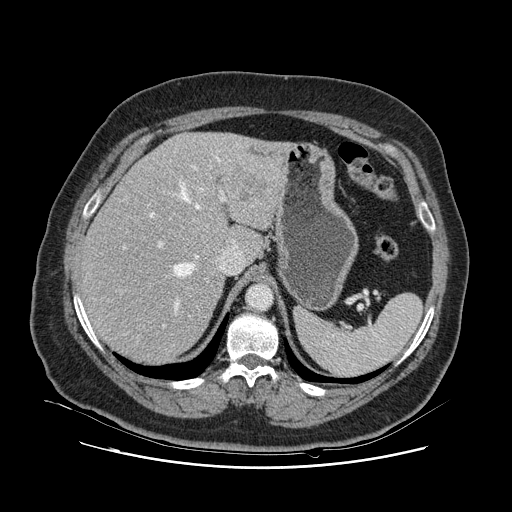
Contrast-enhanced abdominal CT, one axial slice; slice 84 of 132 in the series (ordered by position); 120 kVp; soft-tissue window (W 400 / L 40 HU); 2.5 mm slice thickness; 512 × 512 image matrix. Female patient, age 73 years. Case-level facts recorded for this patient, not image findings: diagnosis: colorectal cancer liver metastases, imaged before liver resection; multiple liver metastases: no; largest metastasis: 7 cm; disease in both lobes: no.
Outlined on this slice (expert manual segmentation):
- hepatic veins: bounding box (x1, y1, x2, y2) in pixels: (126, 155, 235, 312)
- liver: (82, 132, 286, 364)
- planned liver remnant (the part of the liver to remain after resection): (82, 160, 241, 364)
- portal vein (with intrahepatic branches): (123, 166, 226, 327)
- liver metastasis: (234, 168, 268, 201)